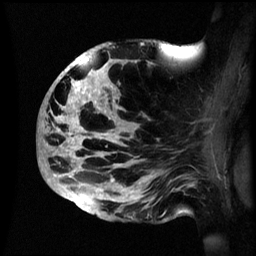
Breast MRI (dynamic contrast-enhanced), one sagittal slice. Slice 32 of 60 in the series (ordered by position). Dynamic contrast-enhanced series, image 2 of 3 at this slice position (ordered by acquisition). 1.5 T. TE 4.2 ms, TR 8.4 ms. 256 × 256 image matrix, field of view 230 × 230 mm. Patient: female, 48 years.
Outlined on this slice (semi-automatic segmentation, software-assisted and operator-edited):
- analysis volume of interest (the breast-tissue region the enhancement analysis was run in; not a lesion): box from (x=39, y=41) to (x=195, y=222) px
- tumour enhancement mask (voxels above the 70 % enhancement threshold inside the analysis volume of interest): (x=39, y=56)–(x=138, y=213)